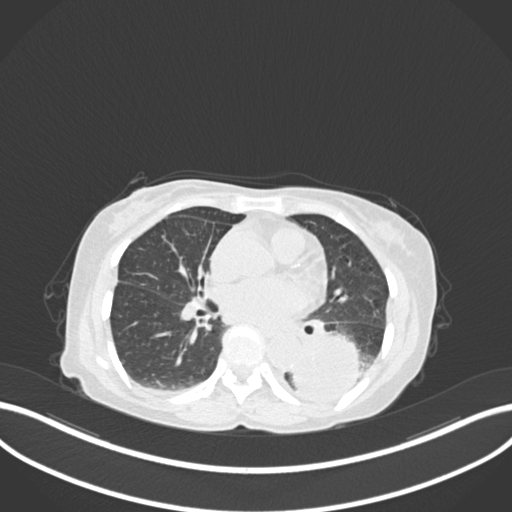
Chest CT, one axial slice. Position 69 of 233 along the scan axis. Lung window (W 1500 / L -600 HU). 1 mm slice thickness. 512 × 512 image matrix, field of view 400 × 400 mm. Patient: female, 78 years. Case-level facts recorded for this patient, not image findings: clinical TNM (as recorded): T3 N0 M1.
Outlined on this slice (bounding box drawn by a radiologist):
- lung tumour (recorded histology: squamous cell carcinoma): bounding box [x1, y1, x2, y2] px = [291, 329, 363, 406]